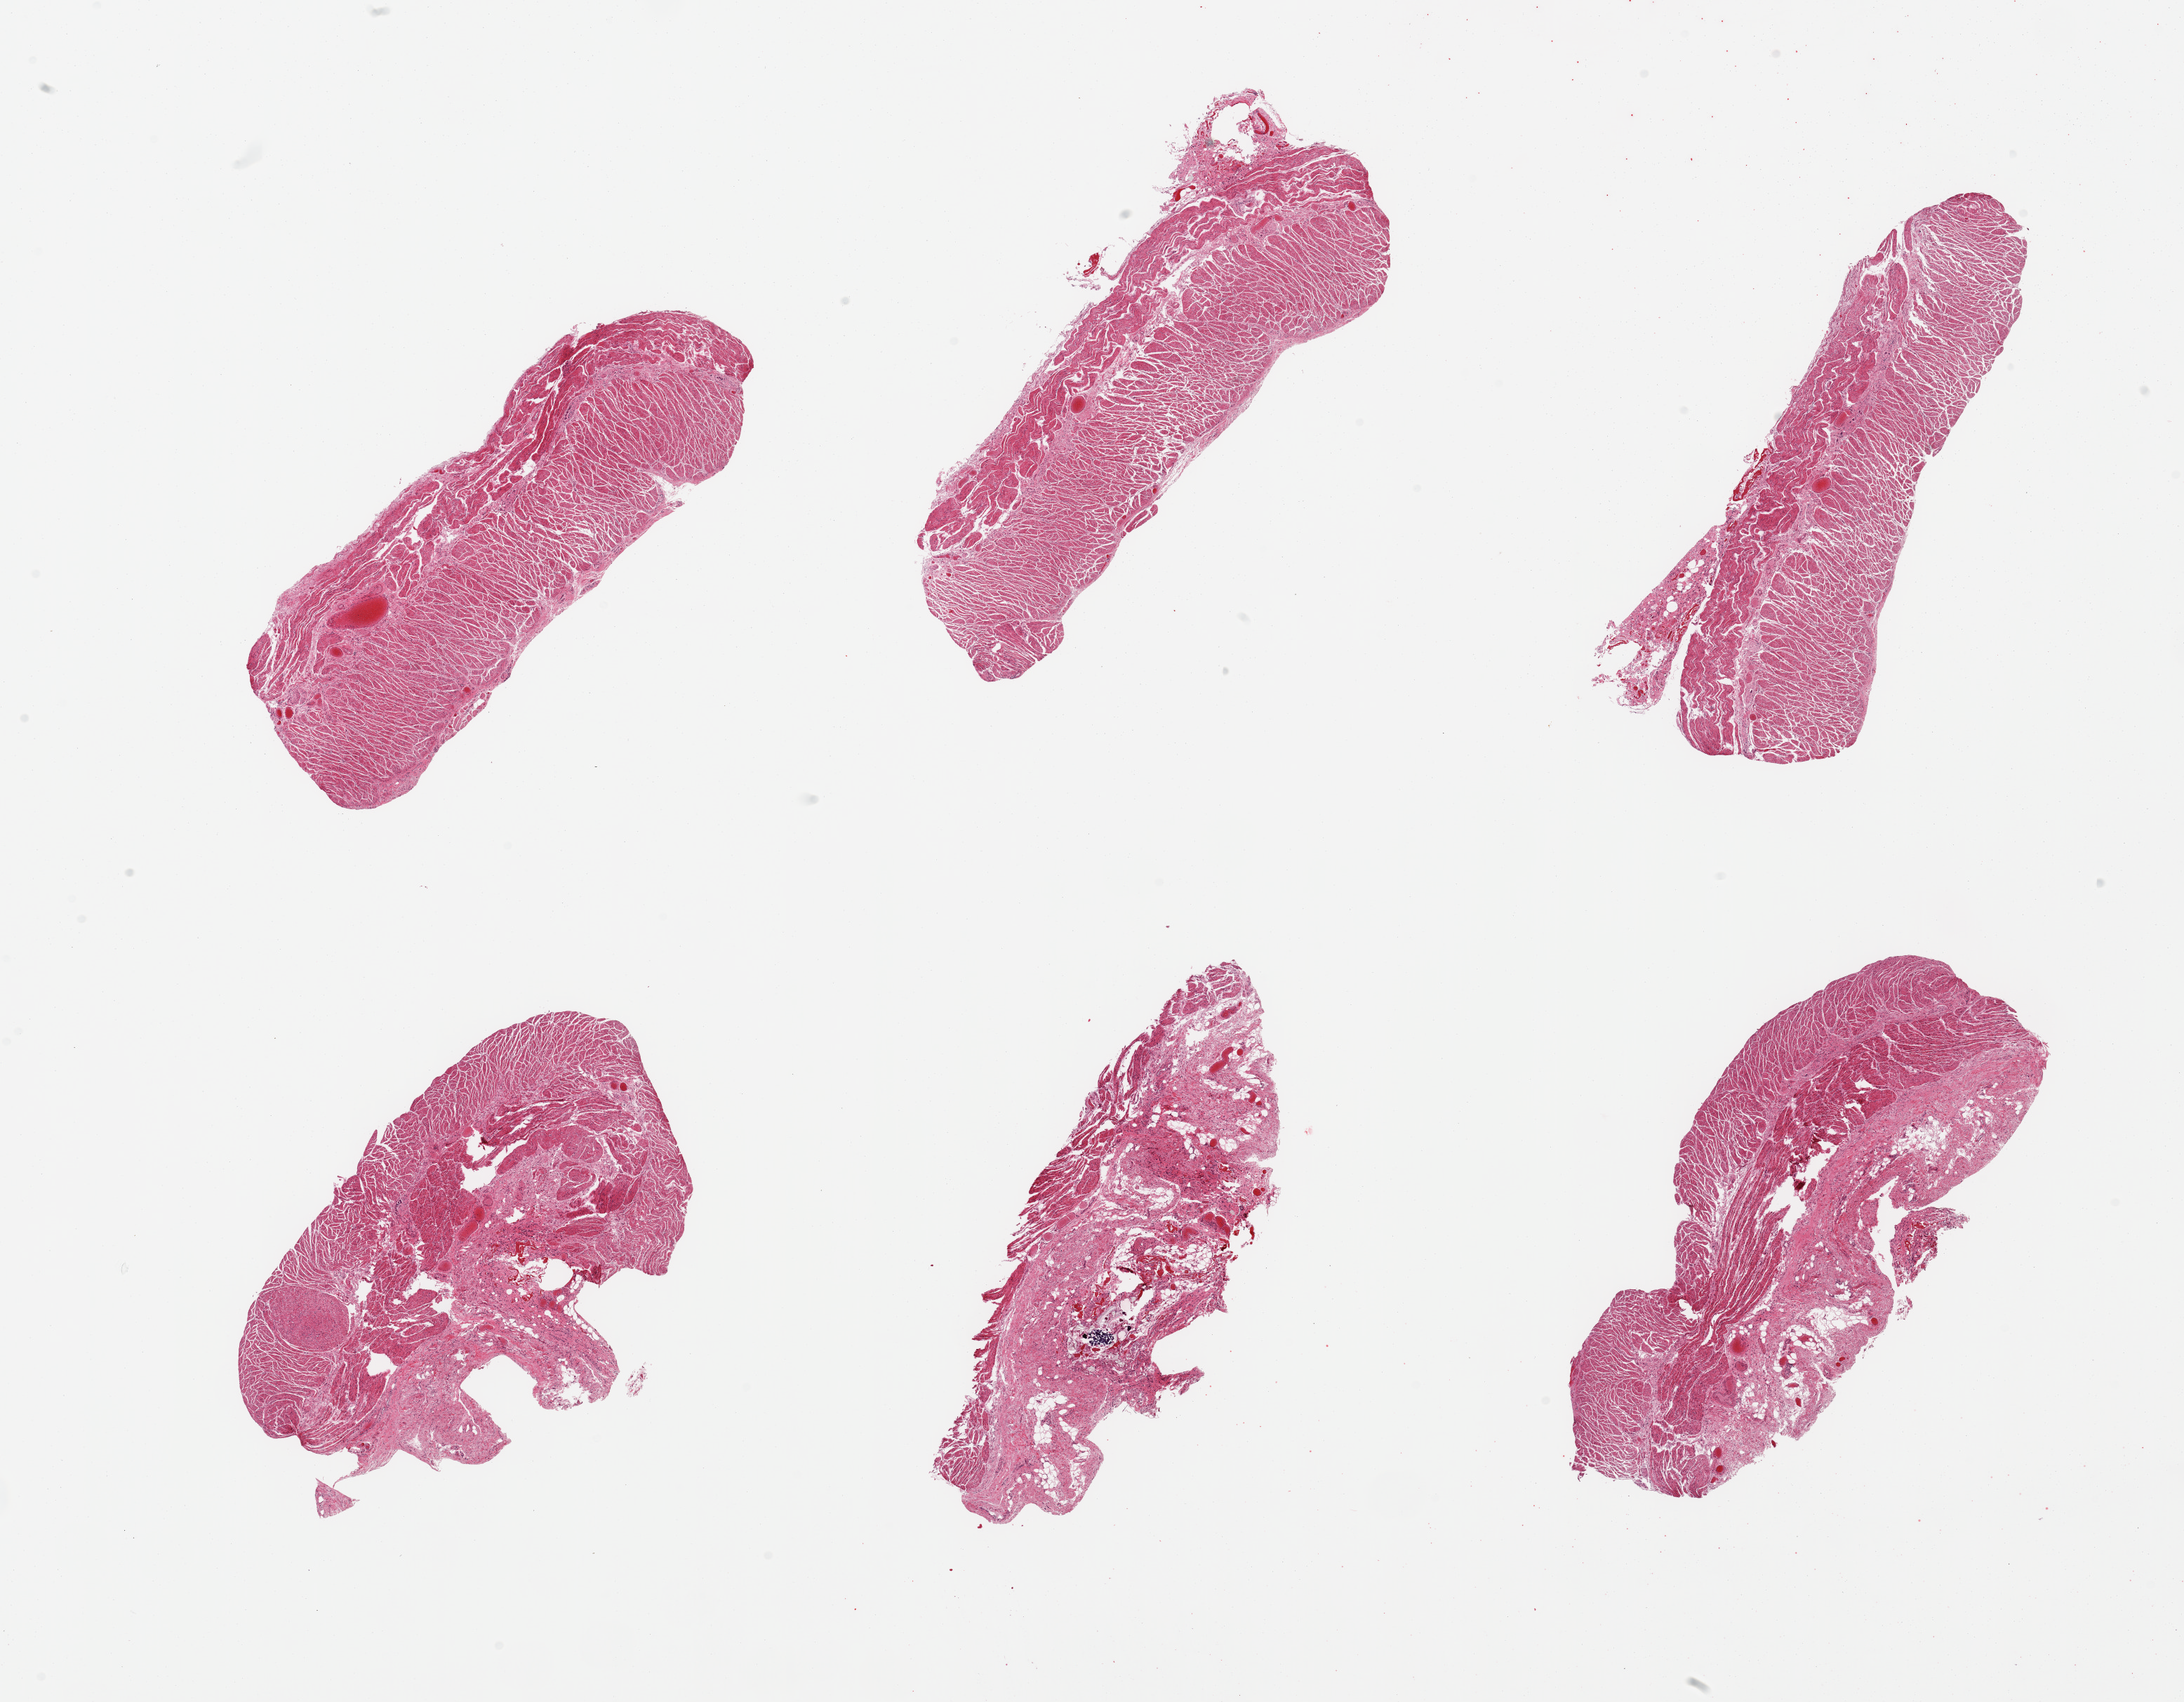
Digitized hematoxylin and eosin (H&E)-stained section, shown as a low-resolution overview of the whole scanned area (about 24.6 x 19.2 mm); PAXgene-fixed paraffin-embedded (PFPE) section; target tissue: gastroesophageal junction; donor tissue sample. Donor sex: female.
Review note (as recorded): 6 pieces; 1 piece is 90% submucosa with embedded ingested food; 2 others have 40% submucosa.